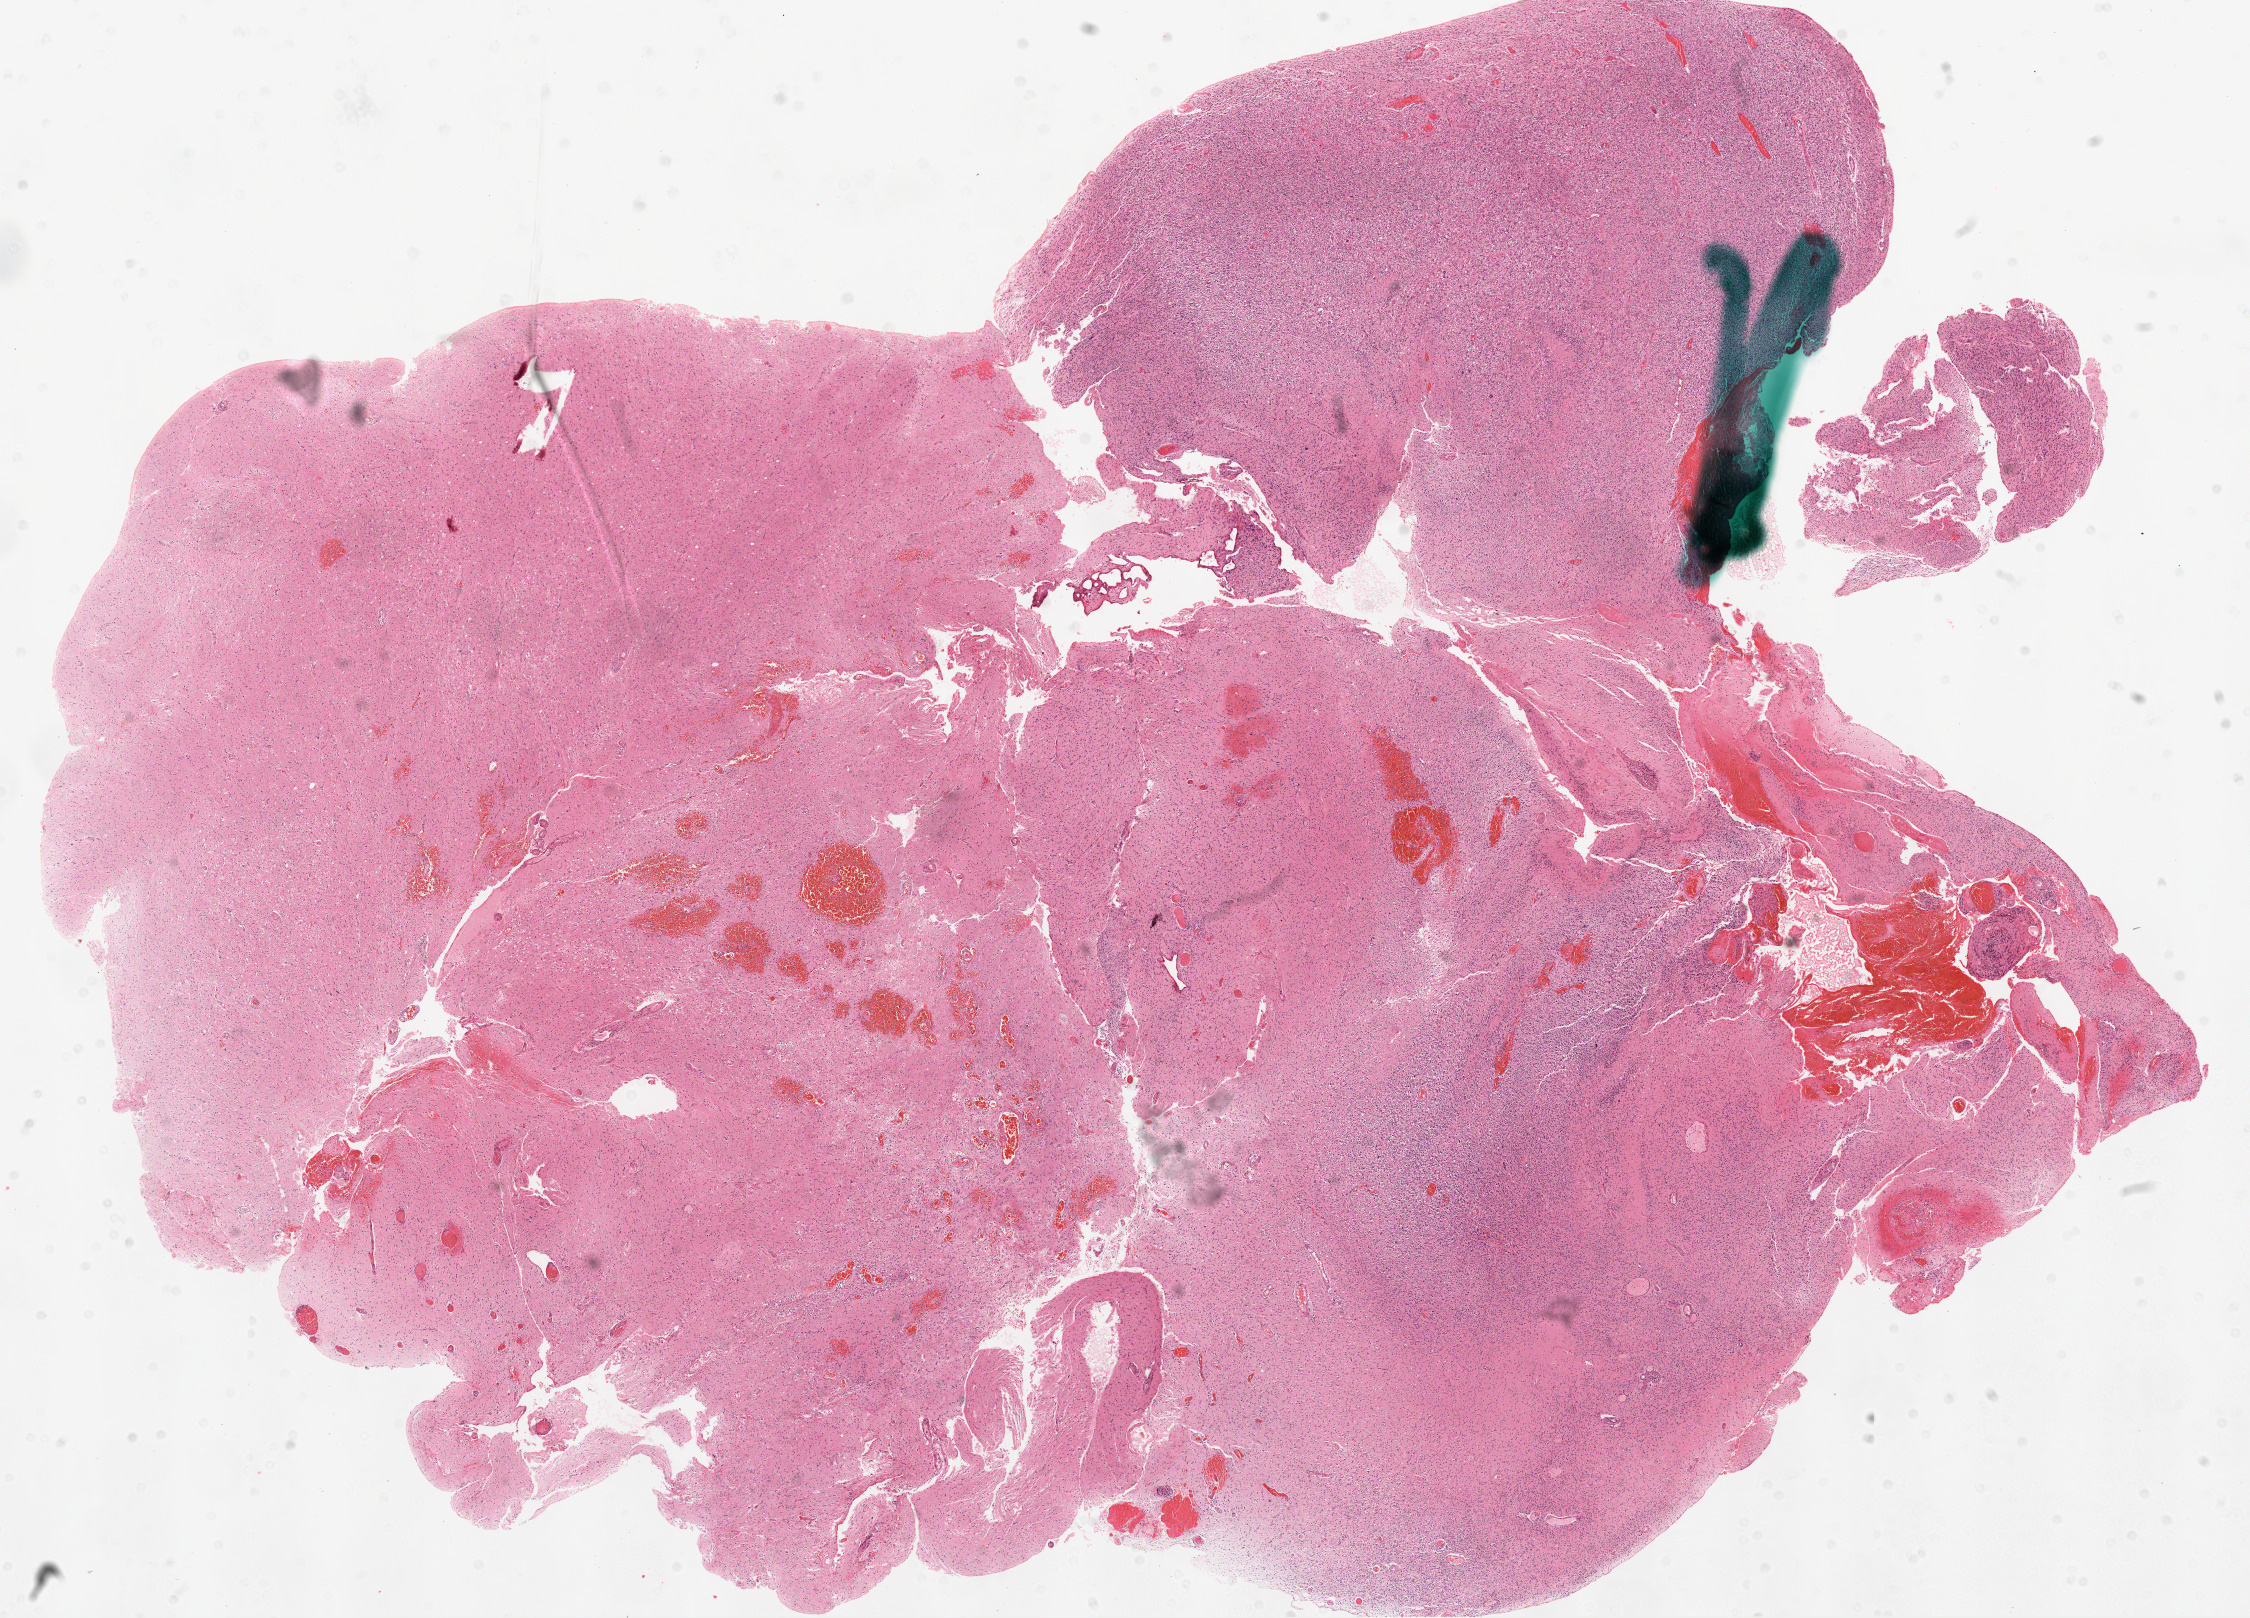
Whole-slide histology image, Hematoxylin and eosin (H&E) stained — low-resolution overview of the scanned area, about 18.1 x 13.0 mm; formalin-fixed paraffin-embedded (FFPE) diagnostic section; brain, primary tumour sample. Female, age 20 years at initial diagnosis.
Diagnosis: Glioblastoma.